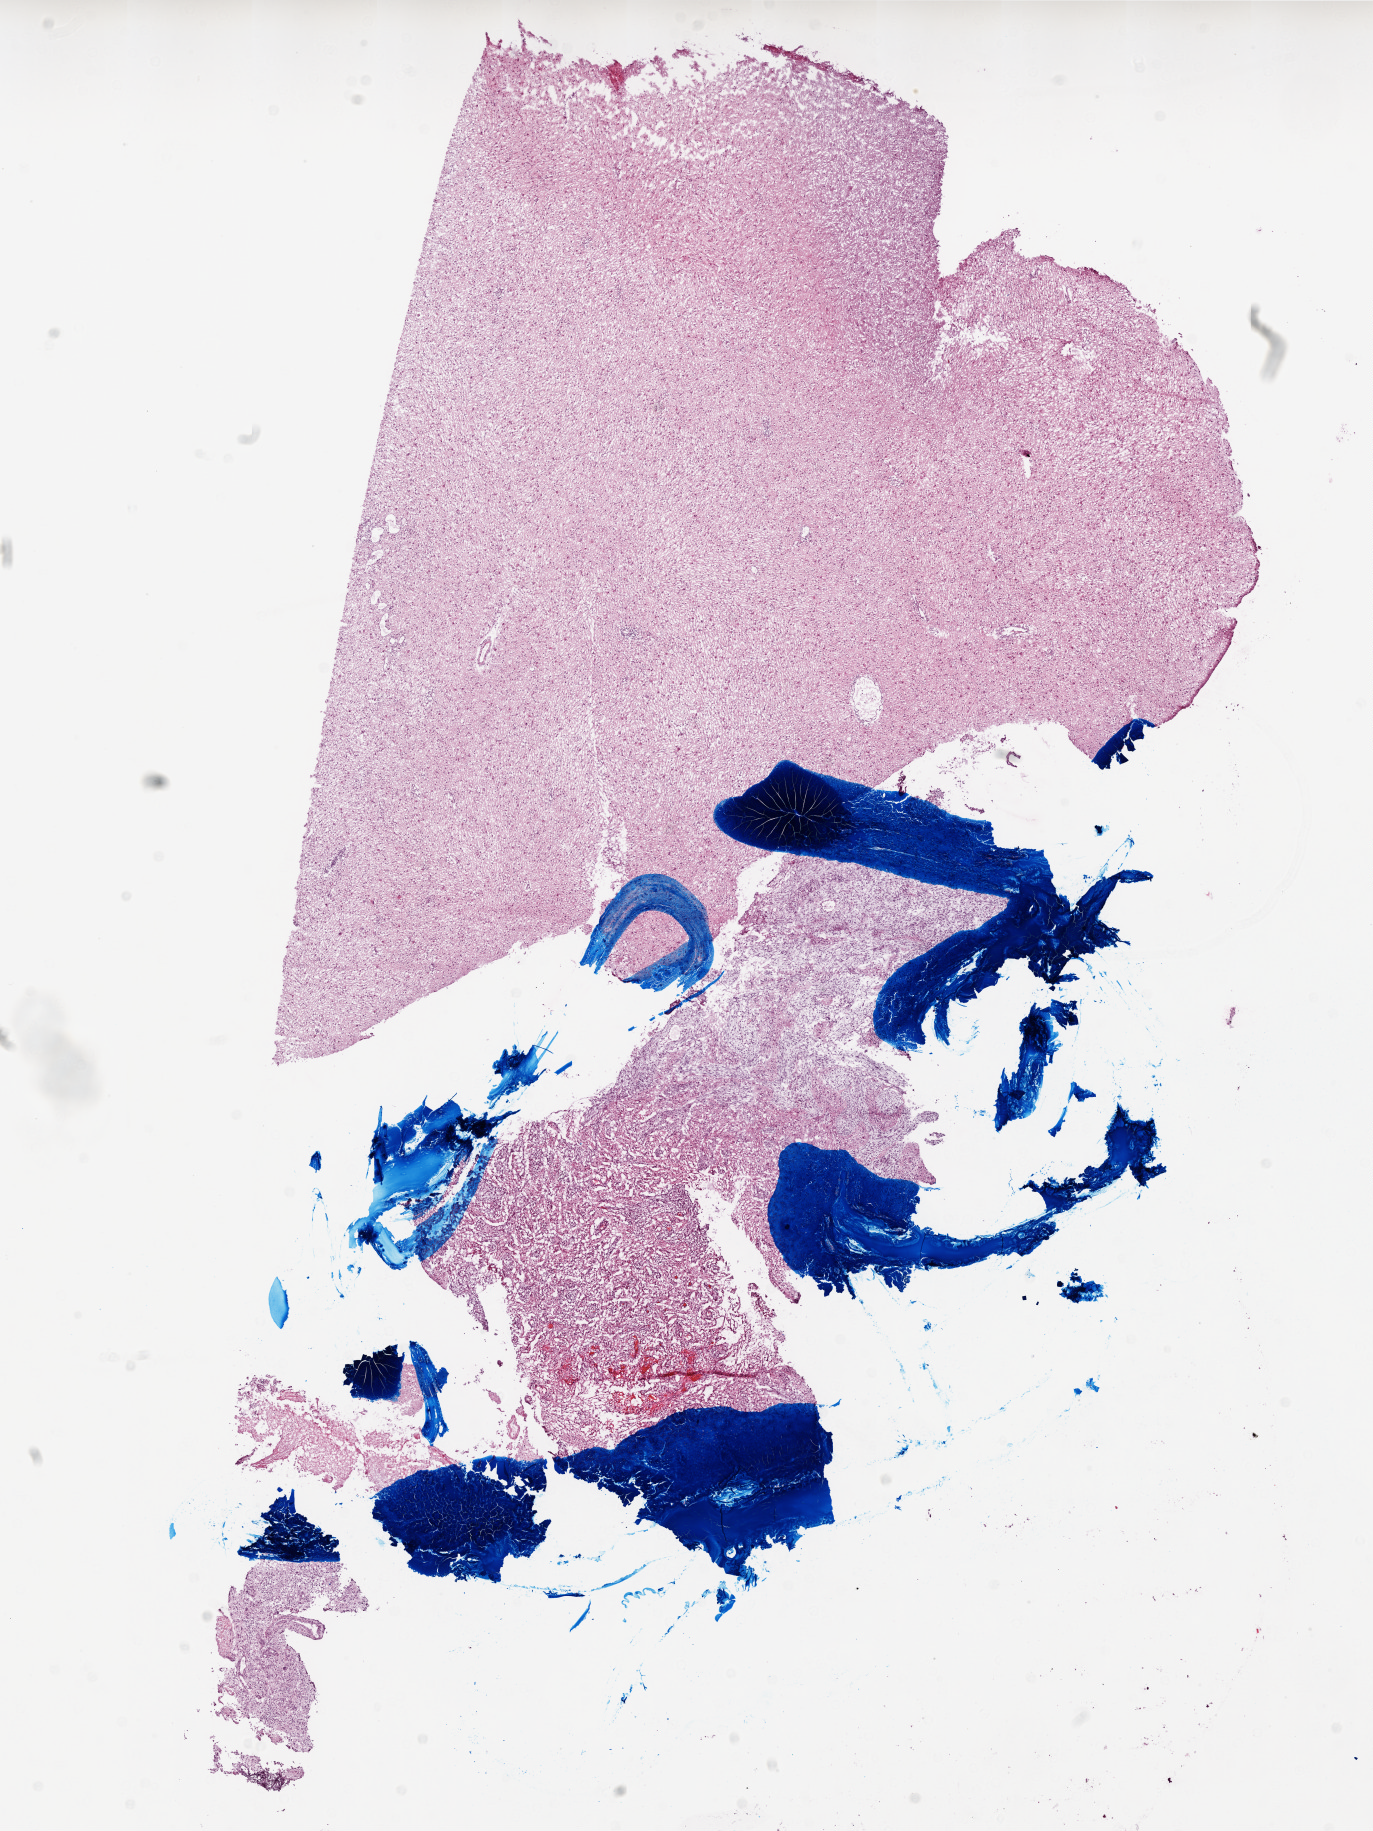
Digitized Hematoxylin and eosin (H&E) stained tissue section (whole slide), whole scanned area (about 11.0 x 14.7 mm) shown as a low-resolution overview, frozen section from the top of the tissue portion, sample: primary tumour, brain. Patient: female, age at initial diagnosis 63 years. Pathologist review of this section (percent, as recorded): tumour cells 75%, tumour nuclei 90%, normal cells 0%, stromal cells 25%, necrosis 0%.
Diagnosis: Glioblastoma.